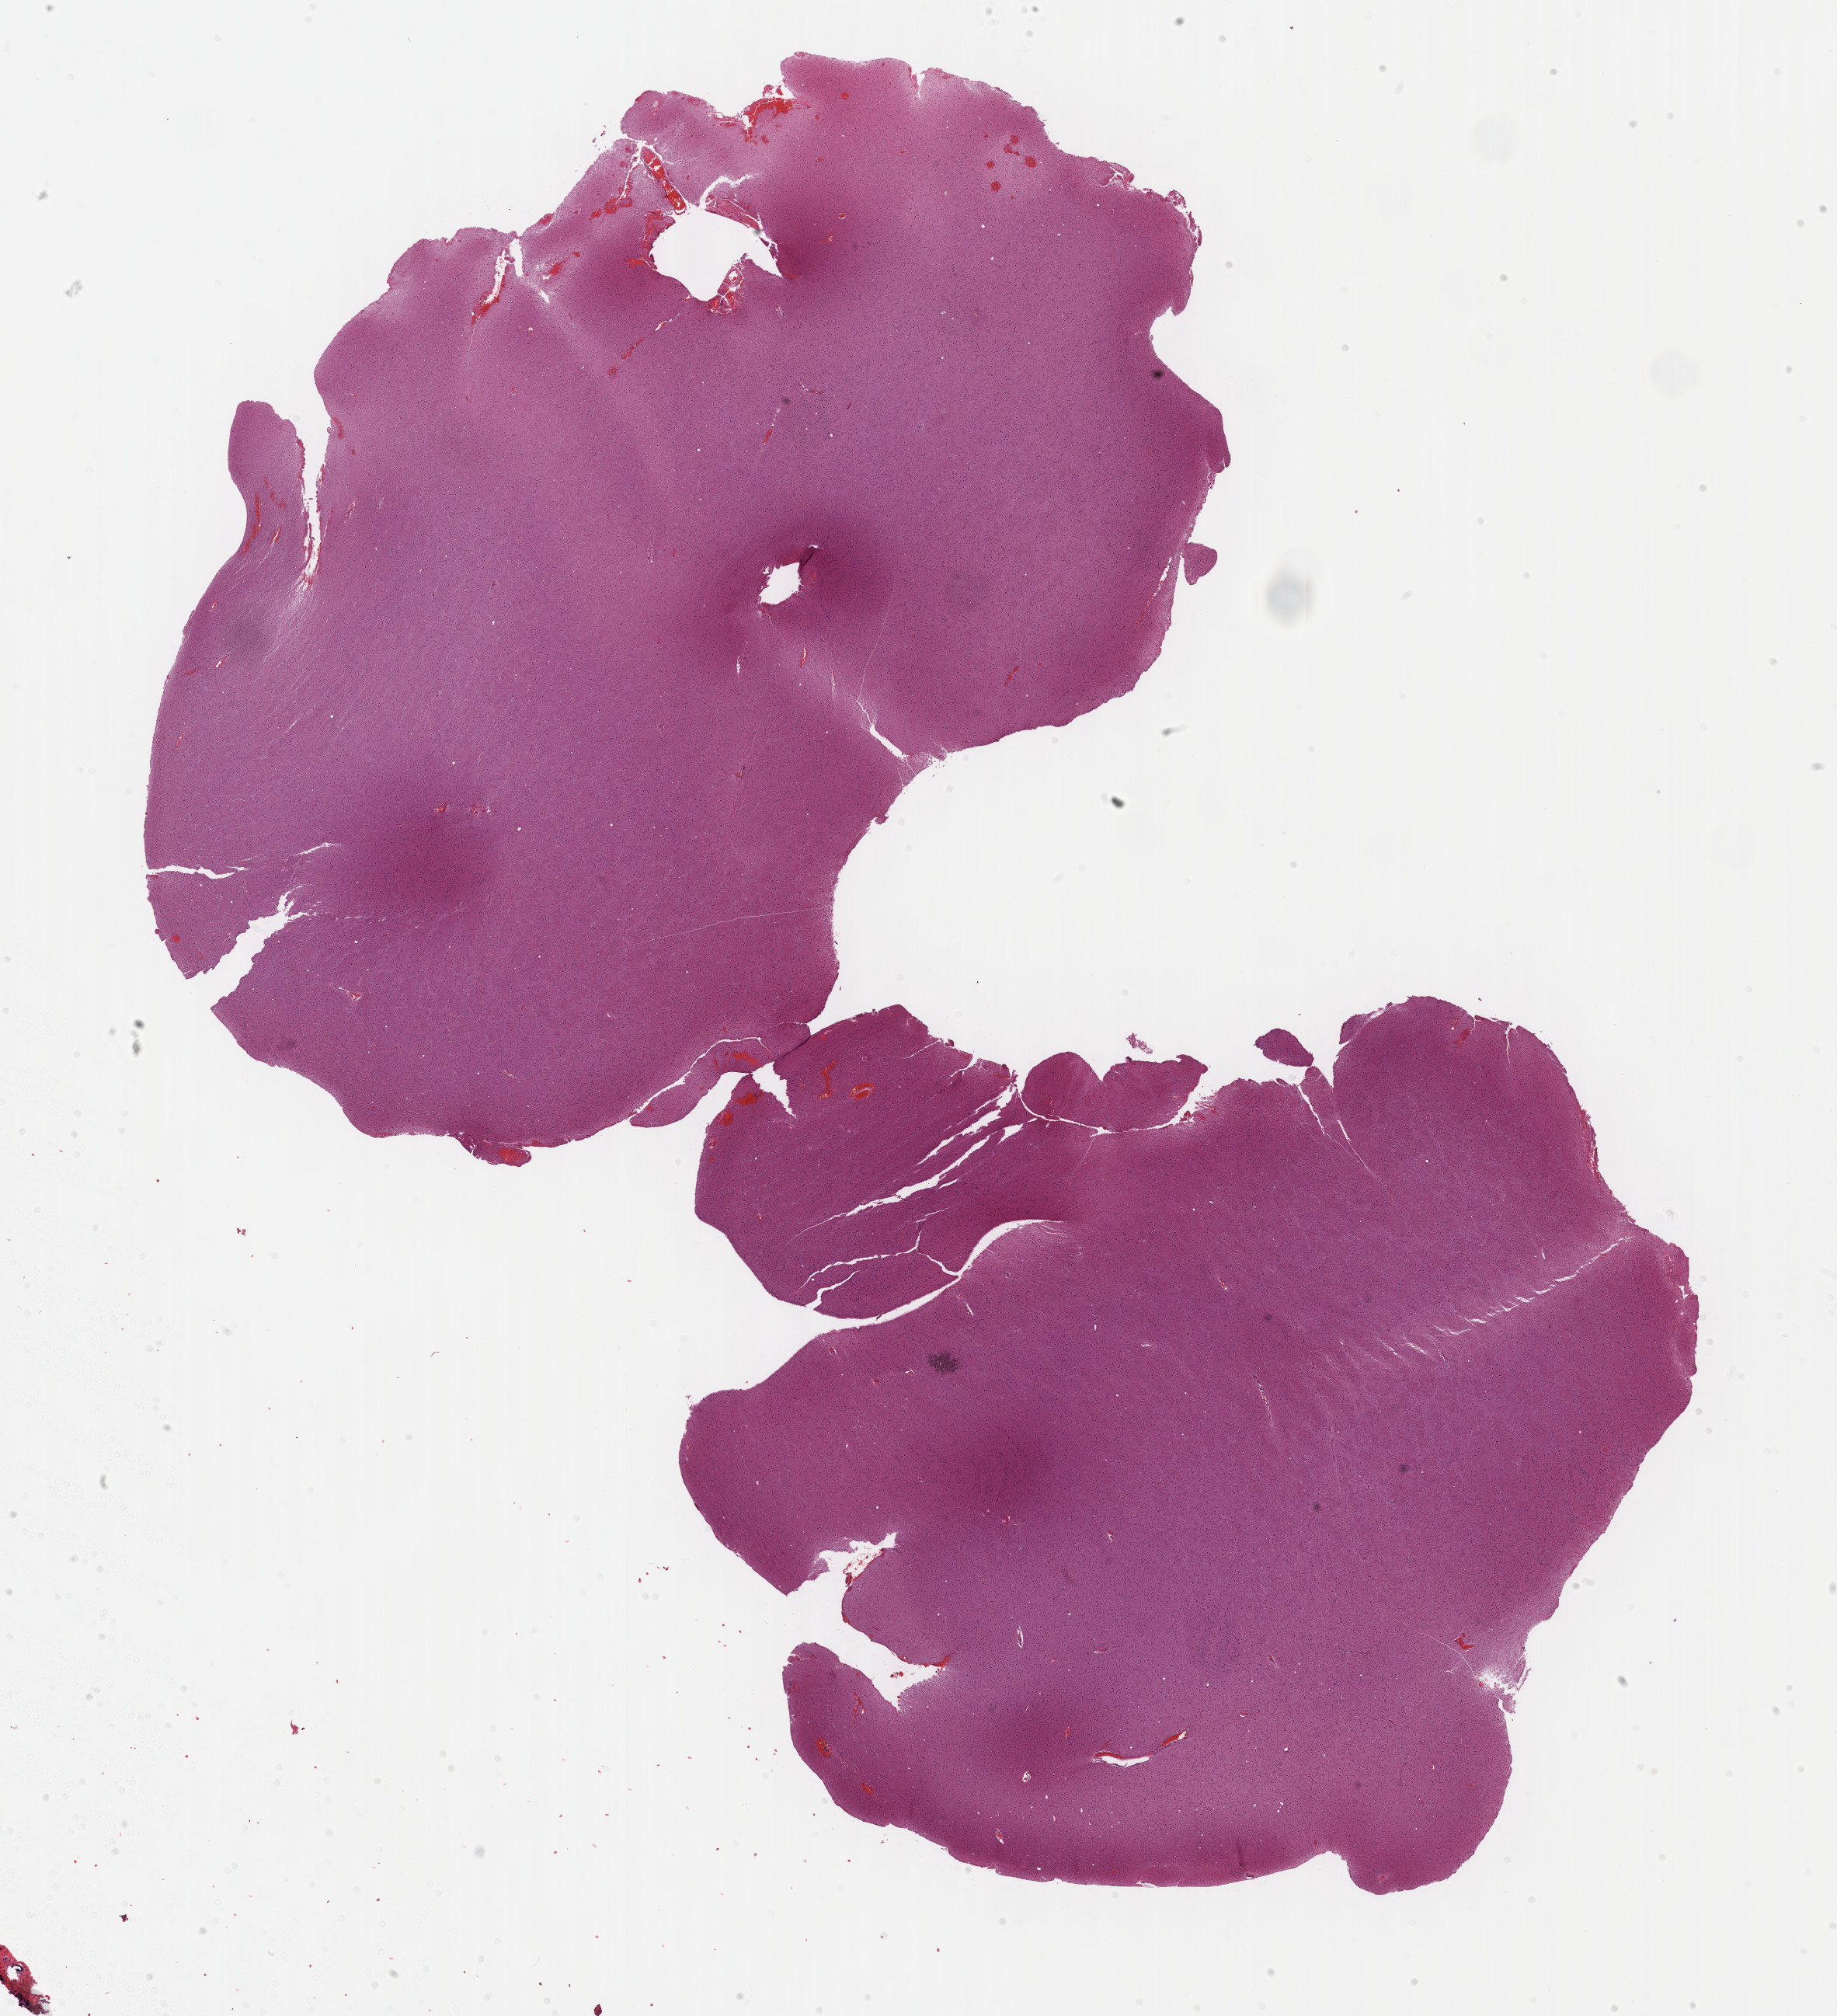
Digitized H&E tissue section (whole slide) — shown as a low-resolution overview of the whole scanned area (about 19.1 x 21.0 mm, slide scanned at 40x), FFPE section, brain, primary tumour sample. Patient: male, age at initial diagnosis 21 years. Histologic grade: G2 (moderately differentiated).
Histologic diagnosis: Oligodendroglioma, NOS. Laterality: right.